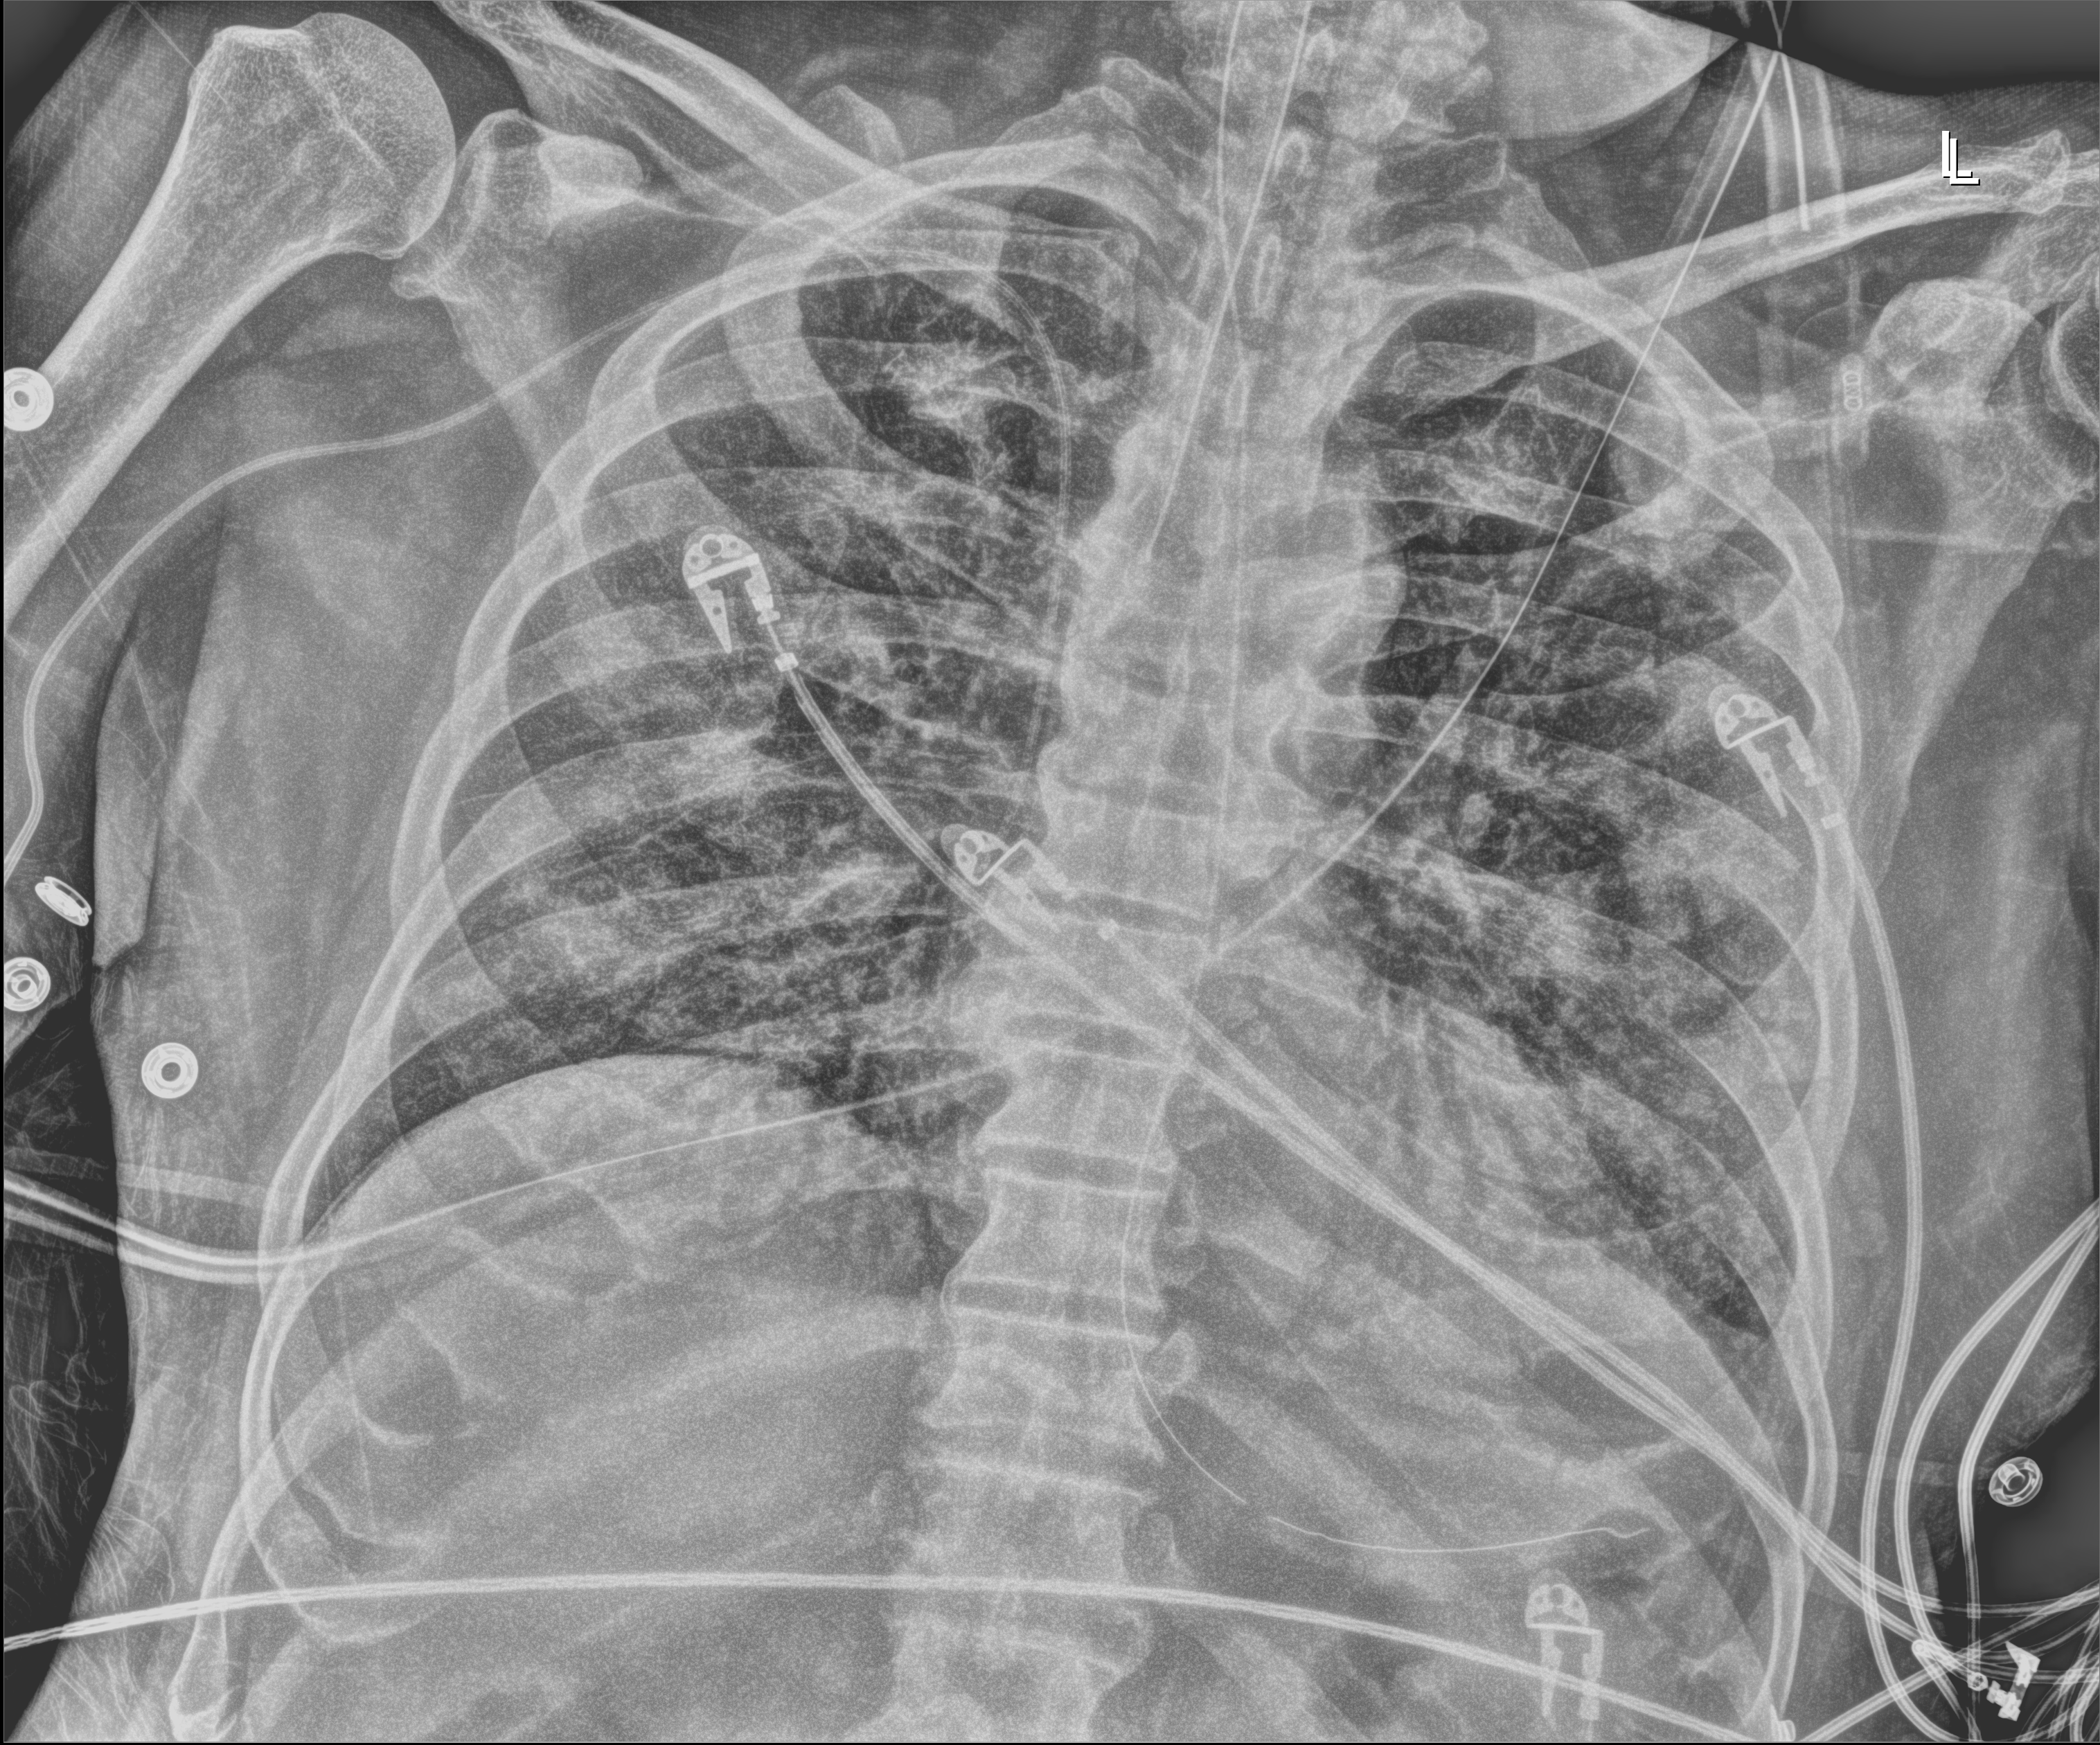
Portable chest radiograph, anteroposterior (AP) projection. Patient hospitalised with COVID-19; male, aged 75–90 years.
Hospital-stay facts (about this admission, not read from this image; timing relative to this image not recorded):
- admitted to intensive care during this hospital stay: yes